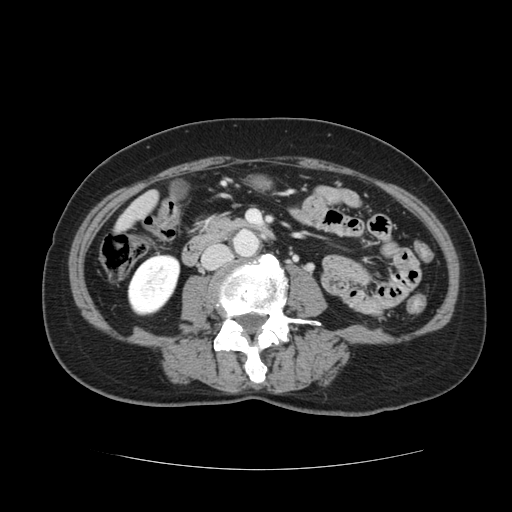
Contrast-enhanced abdominal CT, one axial slice; slice 14 of 128 in the series (ordered by position); 120 kVp; intravenous contrast given; soft-tissue window (W 400 / L 40 HU); 2.5 mm slice thickness; 512 × 512 image matrix. Female patient, age 67 years. Case-level facts recorded for this patient, not image findings: diagnosis: colorectal cancer liver metastases, imaged before liver resection; multiple liver metastases: yes.
Outlined on this slice (outlined manually by an expert reader):
- liver: bounding box [x1, y1, x2, y2] px = [120, 193, 157, 228]
- planned liver remnant (the part of the liver to remain after resection): [120, 206, 143, 228]